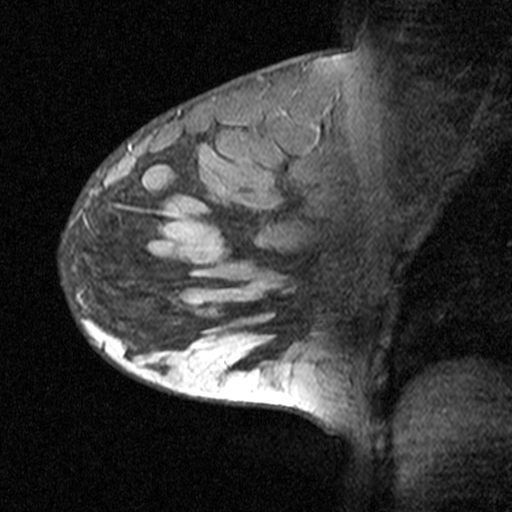
Breast MRI (dynamic contrast-enhanced), one sagittal slice; position 28 of 44 along the scan axis; dynamic contrast-enhanced study with each time point stored as its own series, time point 2 of 3 at this slice position (early post-contrast, ordered by acquisition time); 1.5 T; TE 4.5 ms, TR 11 ms; 512 × 512 image matrix, field of view 200 × 200 mm. Female patient, age 27 years. Case-level facts recorded for this patient, not image findings: setting: breast cancer imaged before/during neoadjuvant chemotherapy; receptor status: HR-positive, HER2-negative.
Annotated regions visible in this slice (semi-automatically segmented with operator editing):
- analysis volume of interest (the breast-tissue region the enhancement analysis was run in; not a lesion): box from (x=61, y=162) to (x=163, y=271) px
- tumour enhancement mask (voxels above the 90 % enhancement threshold inside the analysis volume of interest): (x=93, y=169)–(x=149, y=194)